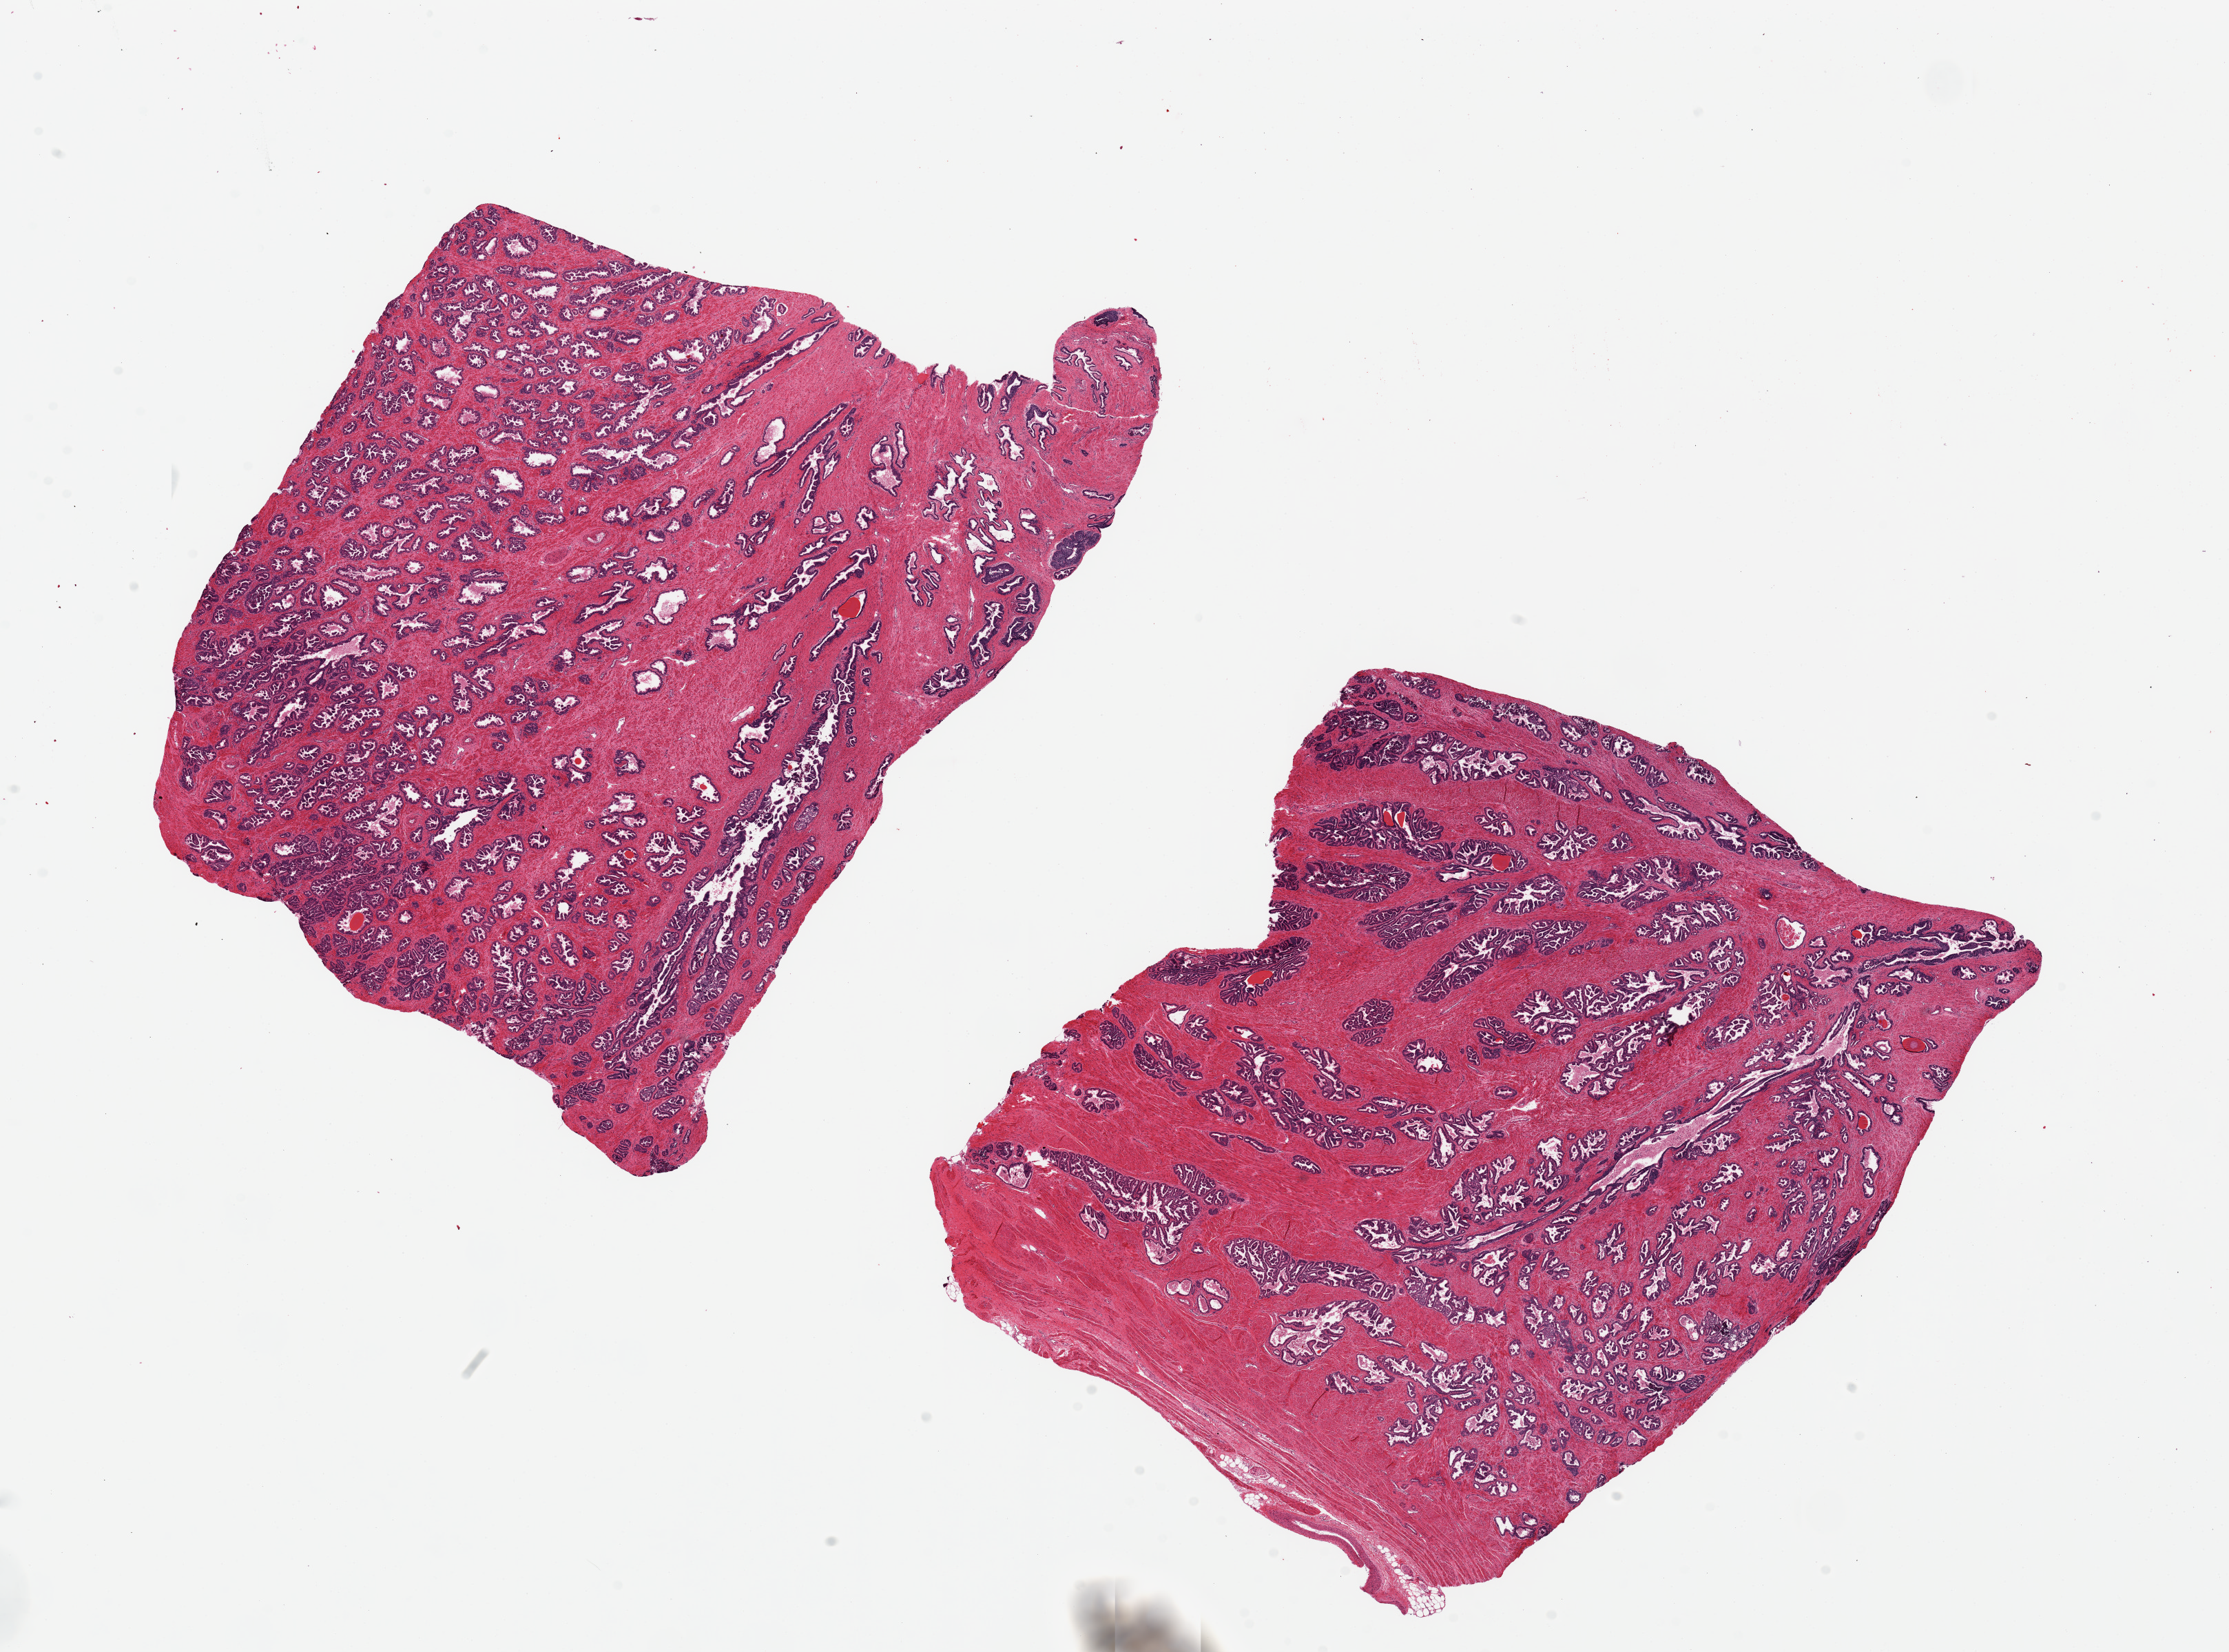
Digitized haematoxylin and eosin-stained section, low-resolution overview of the scanned area, about 25.6 x 19.0 mm (slide scanned at 20x). PAXgene-fixed paraffin-embedded (PFPE) section. Sampled site (target tissue): prostate. Donor tissue sample. Donor: male.
* reviewer comment on this tissue sample: 2 pieces ~ 10x8mm. Diffuse glandular hyperplasia